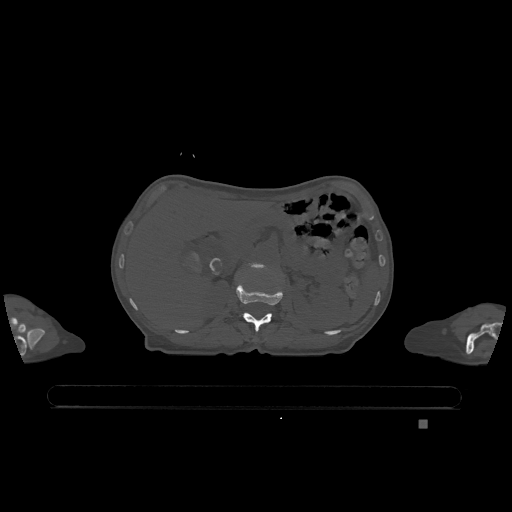
CT including the spine, one axial slice; slice 467 of 1317 in the series (ordered by position); bone window (W 1800 / L 400 HU); 0.5 mm slice thickness; 512 × 512 image matrix, field of view 500 × 500 mm. Female patient, age 74 years. From the clinical record (not read from this slice): primary cancer: lung; vertebrae with lytic lesions (as recorded): T1, T4, T5, T6, L4, L5.
Annotated regions visible in this slice (semi-automatically segmented with operator editing):
- L1 vertebra: bounding box <236,283,283,332> (left, top, right, bottom; pixels)
- L2 vertebra: <253,263,265,270>